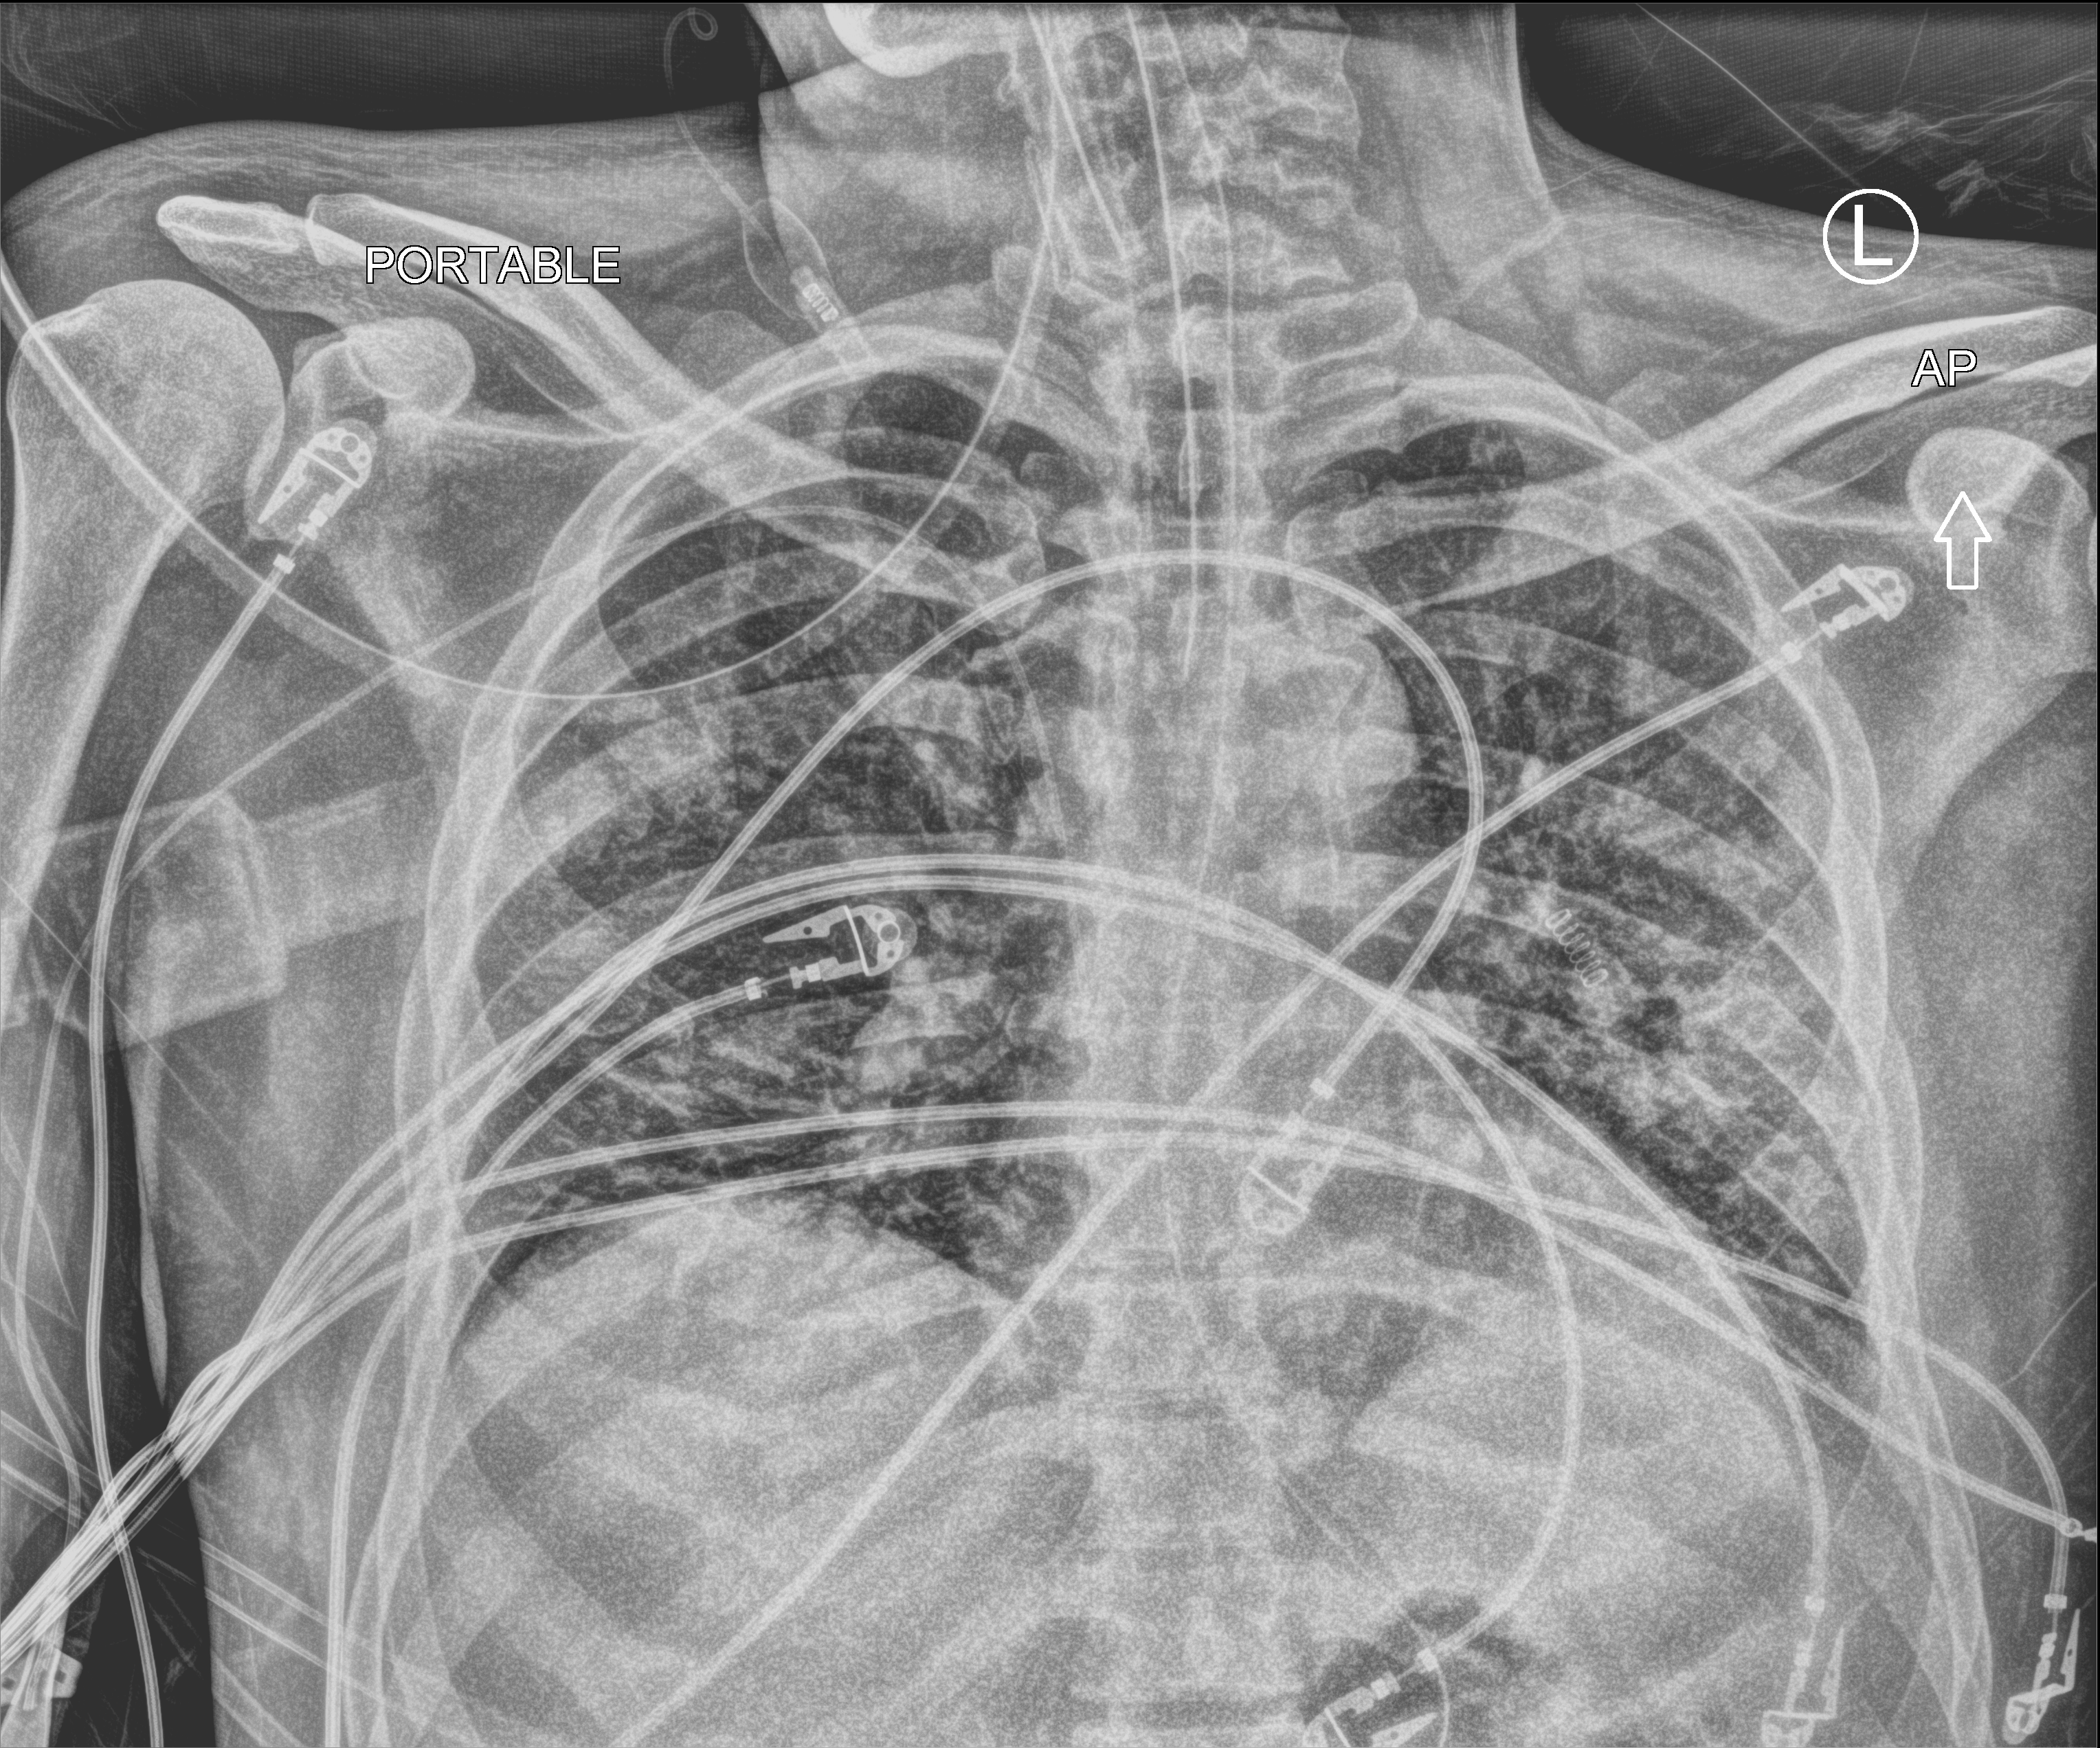
Bedside chest radiograph (computed radiography), anteroposterior (AP) projection. Male patient hospitalised with COVID-19, age 18–59 years.
Admission-level facts for this patient (not findings on this image; timing relative to this image not recorded): mechanically ventilated during this hospital stay: yes; other chronic lung disease (admission record): no; length of hospital stay: 15 days.